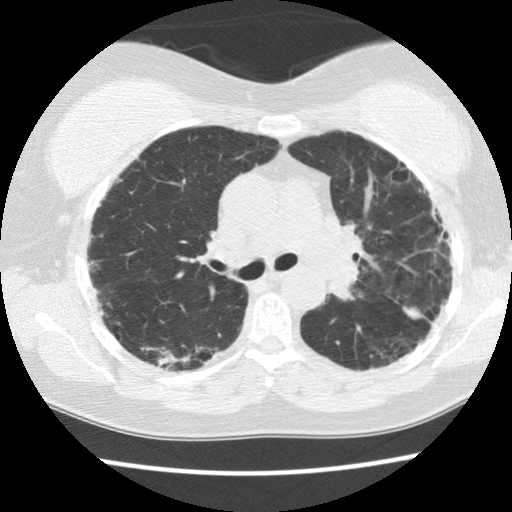
Low-dose screening chest CT, one axial slice; slice 94 of 142 in the series (ordered by position); reconstruction kernel STANDARD; 120 kVp; lung window (W 1500 / L -600 HU); 2.5 mm slice thickness; 512 × 512 image matrix, field of view 320 × 320 mm.
Annotated regions visible in this slice (manually delineated by an expert):
- lesion 1 (tumor): bounding box [x1, y1, x2, y2] px = [404, 307, 422, 319]